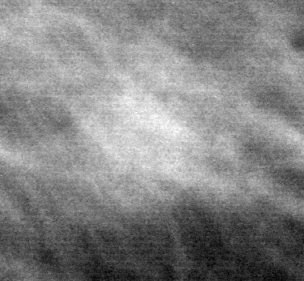
Region of interest cut from a scanned film mammogram (one marked finding), left breast, MLO view, BI-RADS breast density category 1 (scale 1–4).
- Mass, shape oval, margins ill defined; BI-RADS assessment category 5; subtlety rating 2 on a 1 (subtle) to 5 (obvious) scale; pathology result (as recorded, not read from the image): malignant.